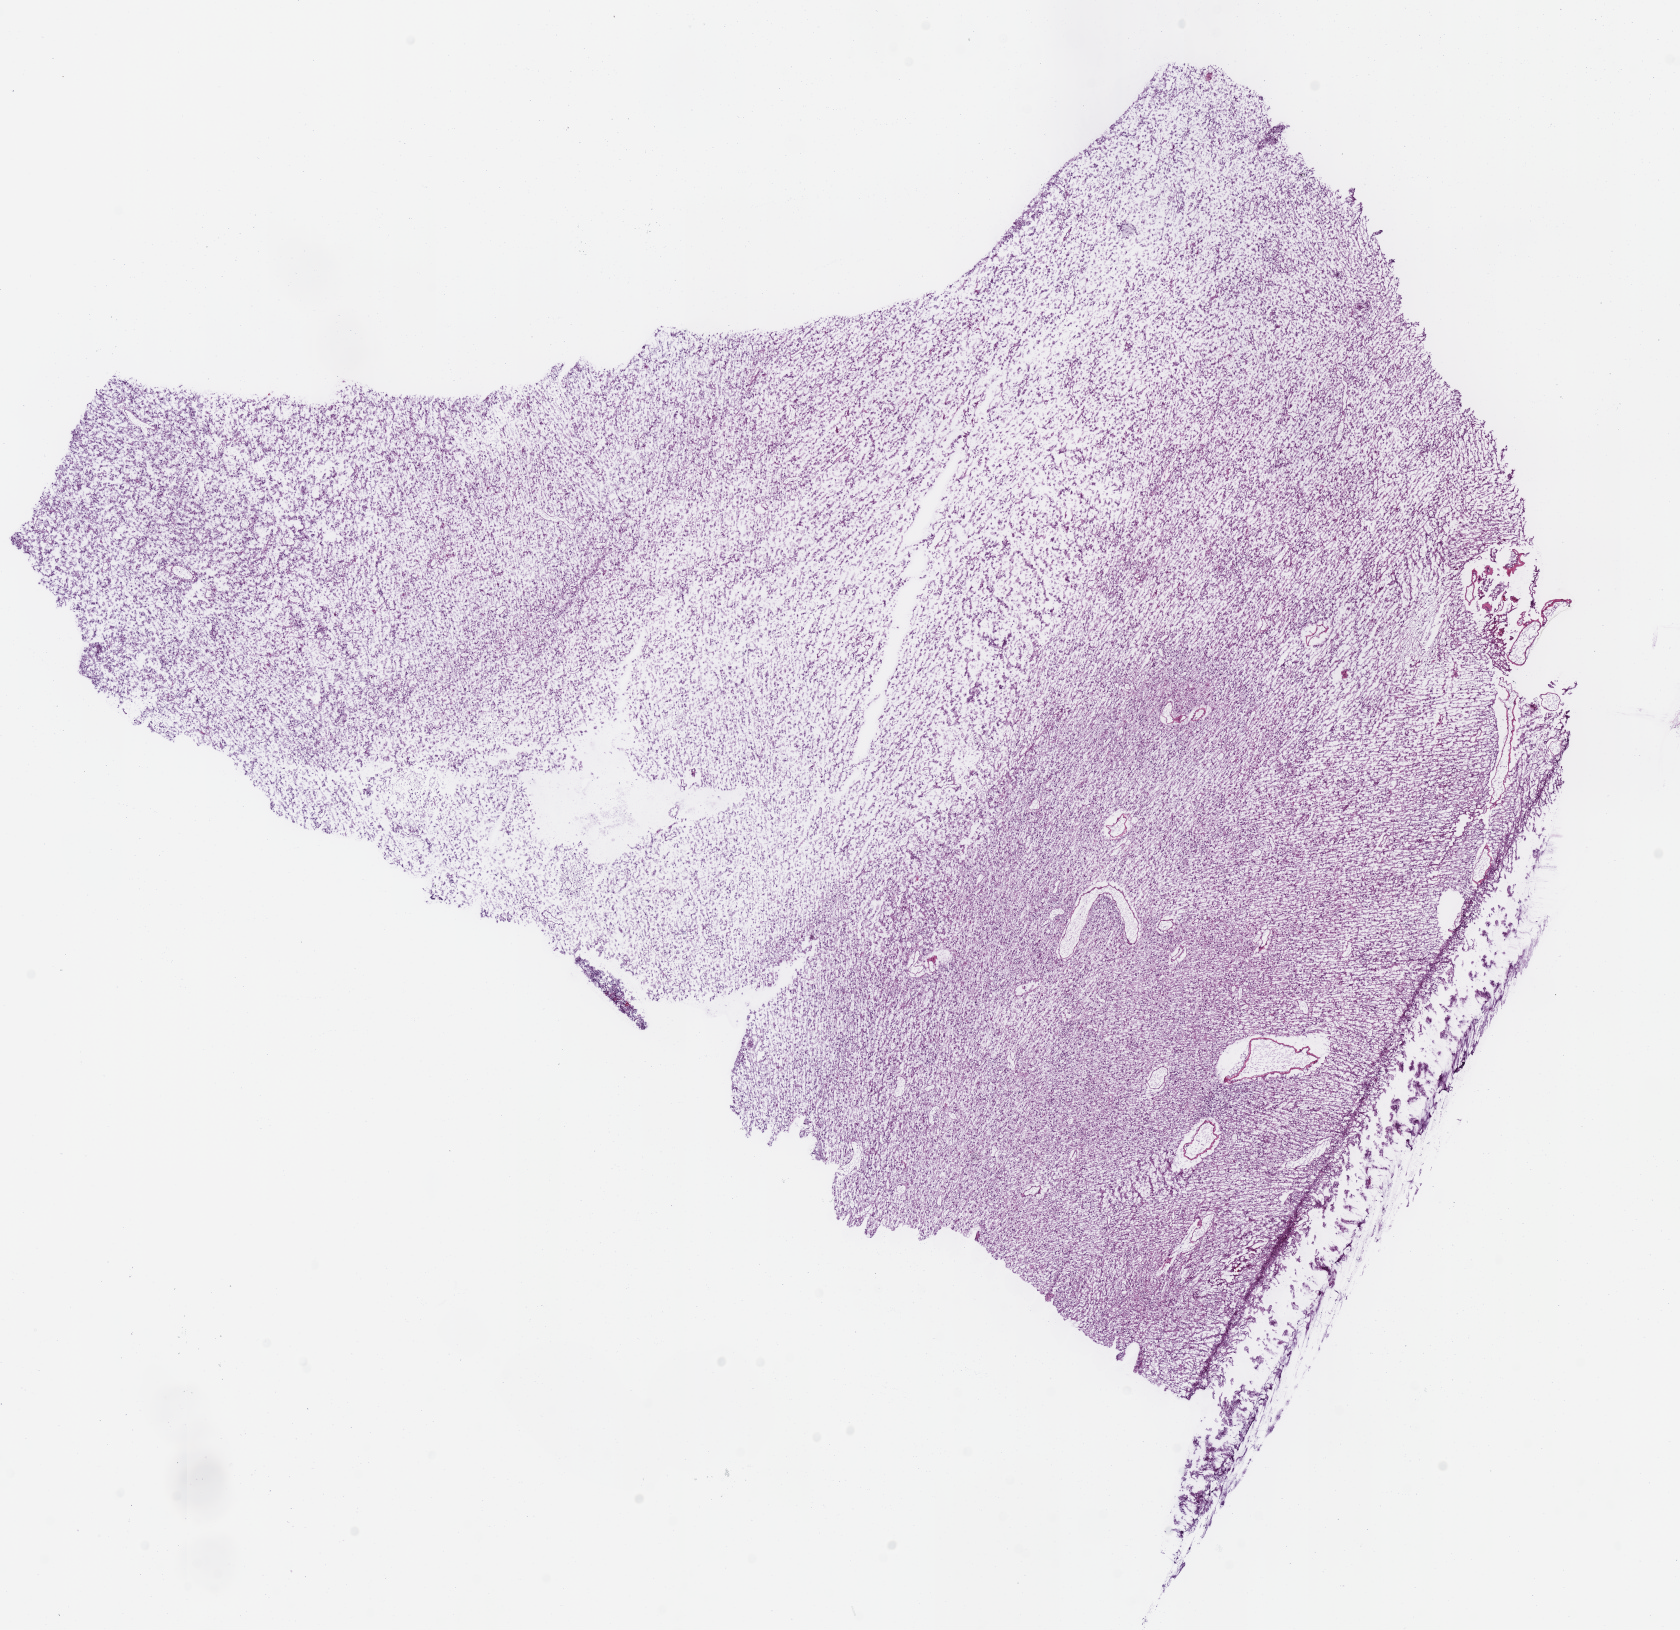
Digitized Hematoxylin and eosin (H&E) stained tissue section (whole slide), shown as a low-resolution overview of the whole scanned area (about 13.2 x 12.8 mm); frozen section from the bottom of the tissue portion; sample: primary tumour, brain. Male patient; age at initial diagnosis 31 years. Histologic grade: G3 (poorly differentiated). Pathologist review of this section (percent, as recorded): tumour cells 100%, tumour nuclei 85%, normal cells 0%, stromal cells 0%, necrosis 0%.
Laterality: left. Diagnosis: Astrocytoma, NOS (cerebrum).